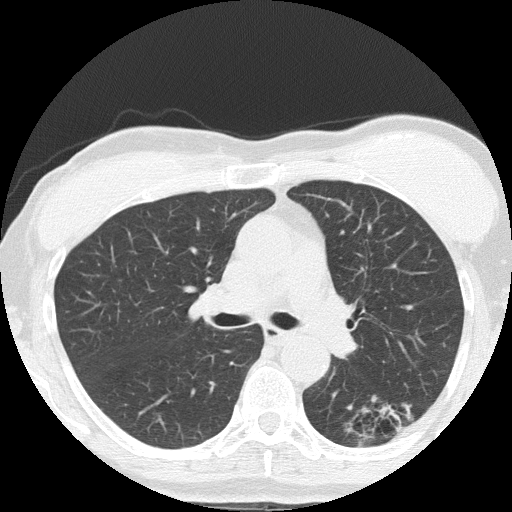
Axial slice from a low-dose chest CT screening exam; third annual screen; lung window (W 1500 / L -600 HU); 2 mm slice thickness; slice 60 of 152 in the series; 512 × 512 image matrix. Female participant, aged 64 years at enrolment. Former smoker at enrolment.
Expert-annotated lung lesion, bounding box <350,382,437,452> (left, top, right, bottom; pixels). The screening reader recorded 3 non-calcified nodules or masses ≥4 mm on this exam; which of them this box marks is not recorded. Official screen result: positive, other. Participant outcome: lung cancer diagnosed 212 days after this screen — adenocarcinoma, NOS, left lower lobe, moderately differentiated (G2), stage IA (AJCC 6th edition), 17 mm at pathology.